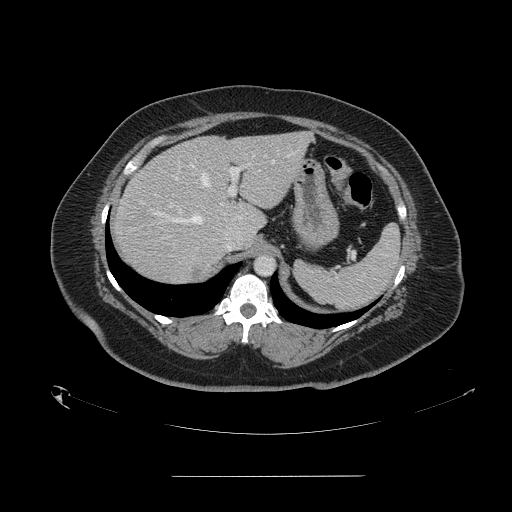
Contrast-enhanced abdominal CT, one axial slice; slice 110 of 164 in the series (ordered by position); 120 kVp; intravenous contrast given; soft-tissue window (W 400 / L 40 HU); 2.5 mm slice thickness; 512 × 512 image matrix, field of view 495 × 495 mm. Female patient, age 52 years. From the clinical record (not read from this slice): diagnosis: colorectal cancer liver metastases, imaged before liver resection; multiple liver metastases: yes; largest metastasis: 3.5 cm; disease in both lobes: no.
Structures marked on this image (manually delineated by an expert):
- hepatic veins: bounding box <156,153,293,223> (left, top, right, bottom; pixels)
- liver: <113,133,310,285>
- planned liver remnant (the part of the liver to remain after resection): <172,133,311,230>
- portal vein (with intrahepatic branches): <170,163,250,213>
- liver metastasis: <193,269,202,277>